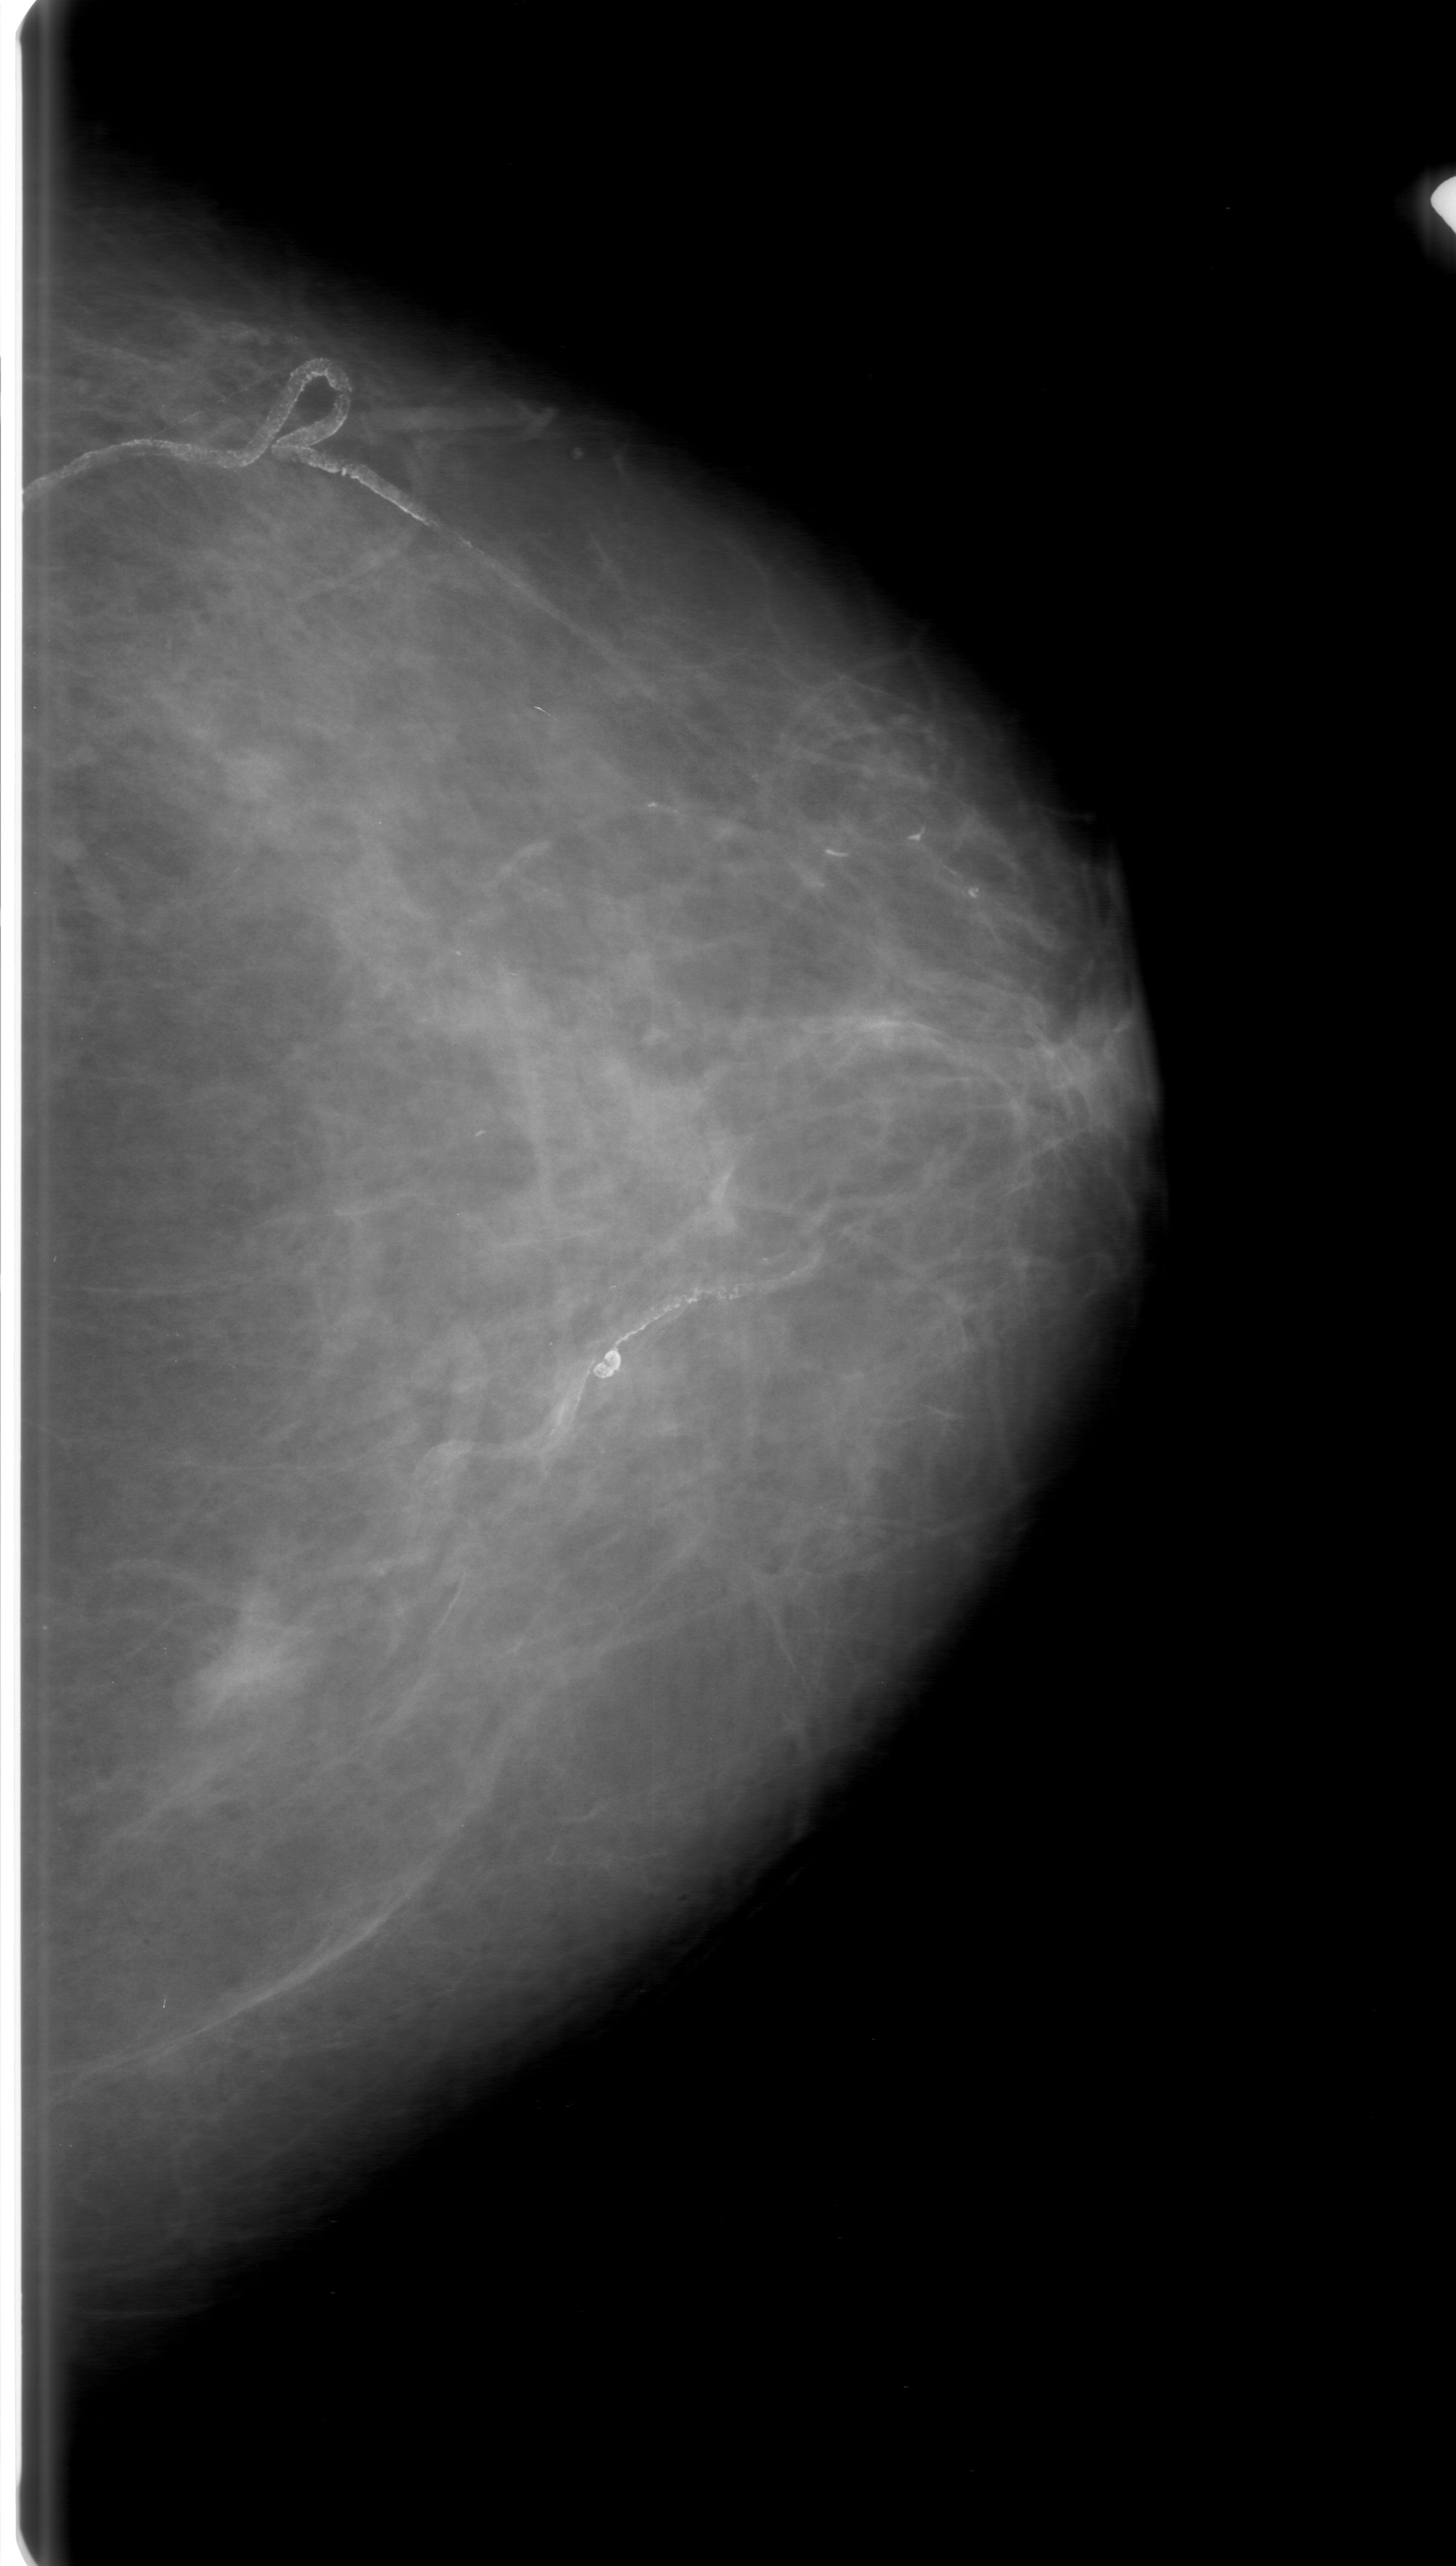
Scanned film-screen mammogram; left breast; CC view; breast composition: scattered fibroglandular densities (BI-RADS density category 2 of 4).
Radiologist-marked abnormalities on this image: mass, shape irregular, margins spiculated; BI-RADS assessment category 3; pathology (as recorded): malignant.